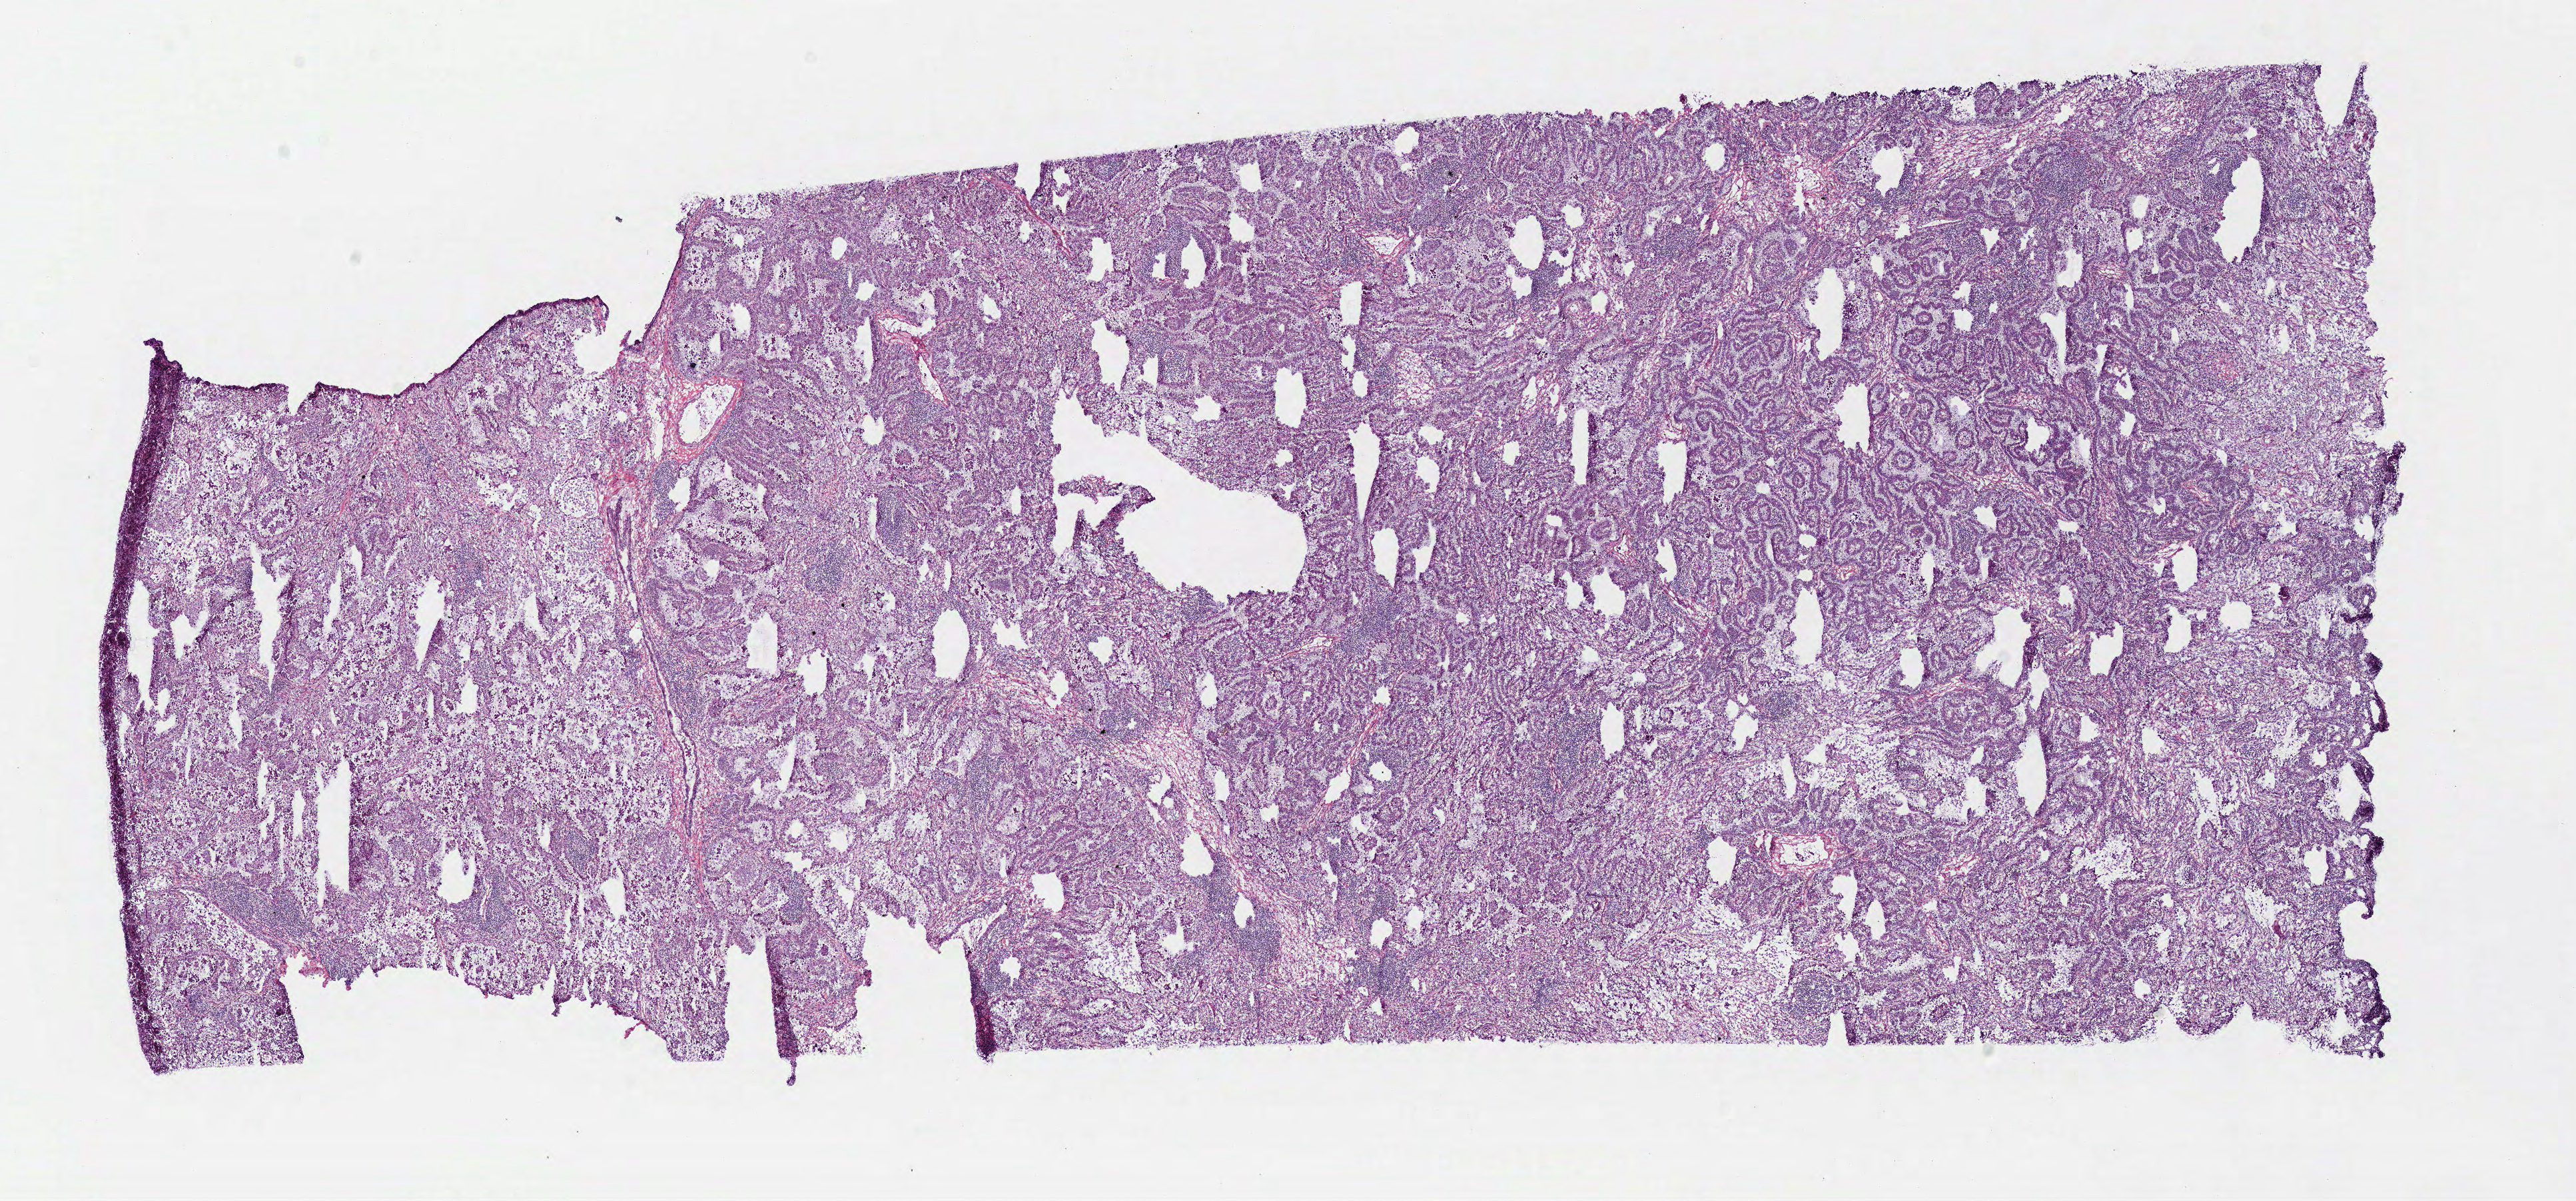
H&E whole-slide image — a low-resolution overview of the entire scanned area, about 15.2 x 7.1 mm; frozen section from the bottom of the tissue portion; sample: primary tumour, lung. Female patient. Slide review estimates, as recorded: tumour cells 100%, tumour nuclei 80%, normal cells 0%, stromal cells 0%, necrosis 0%. Infiltration values recorded for this section: lymphocyte infiltration 12%, monocyte infiltration 3%, neutrophil infiltration 2%.
Pathologic diagnosis: Invasive micropapillary carcinoma (lower lobe, lung). AJCC pathologic stage: IIB (6th edition).